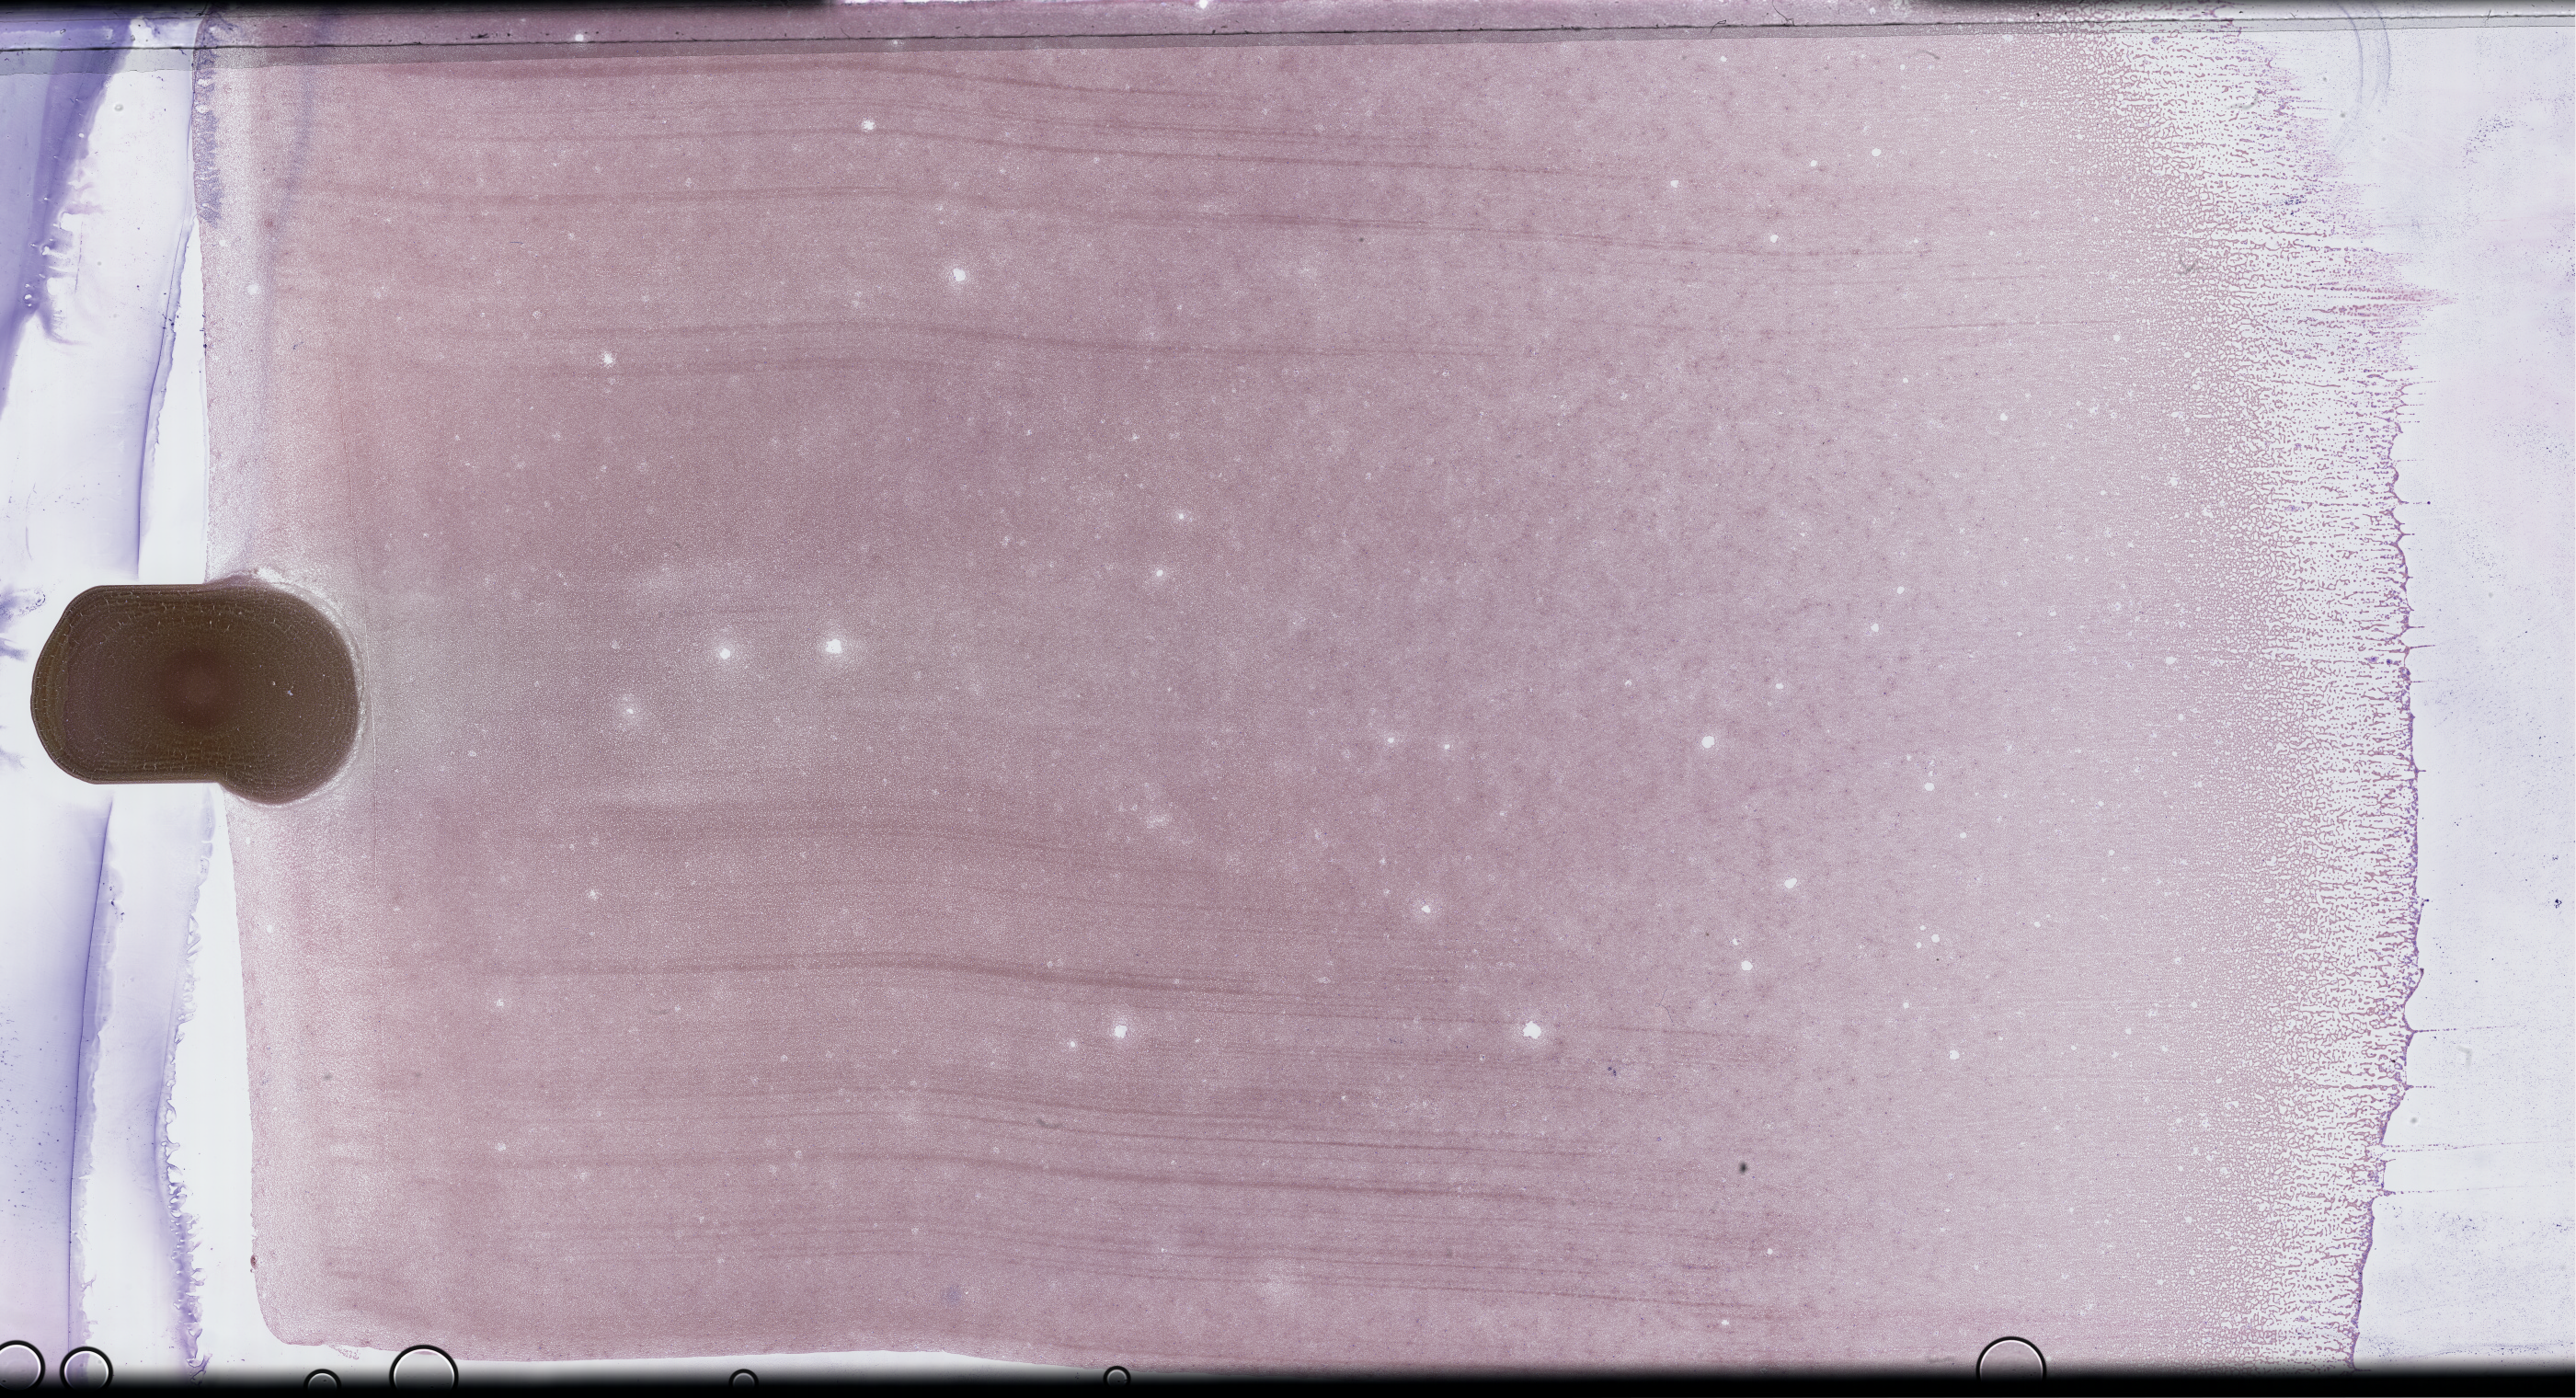
Wright-Giemsa-stained bone marrow smear, whole-slide image — whole scanned area (about 45.2 x 24.5 mm) shown as a low-resolution overview. Patient: male.
Patient diagnosis: Plasma Cell Myeloma.